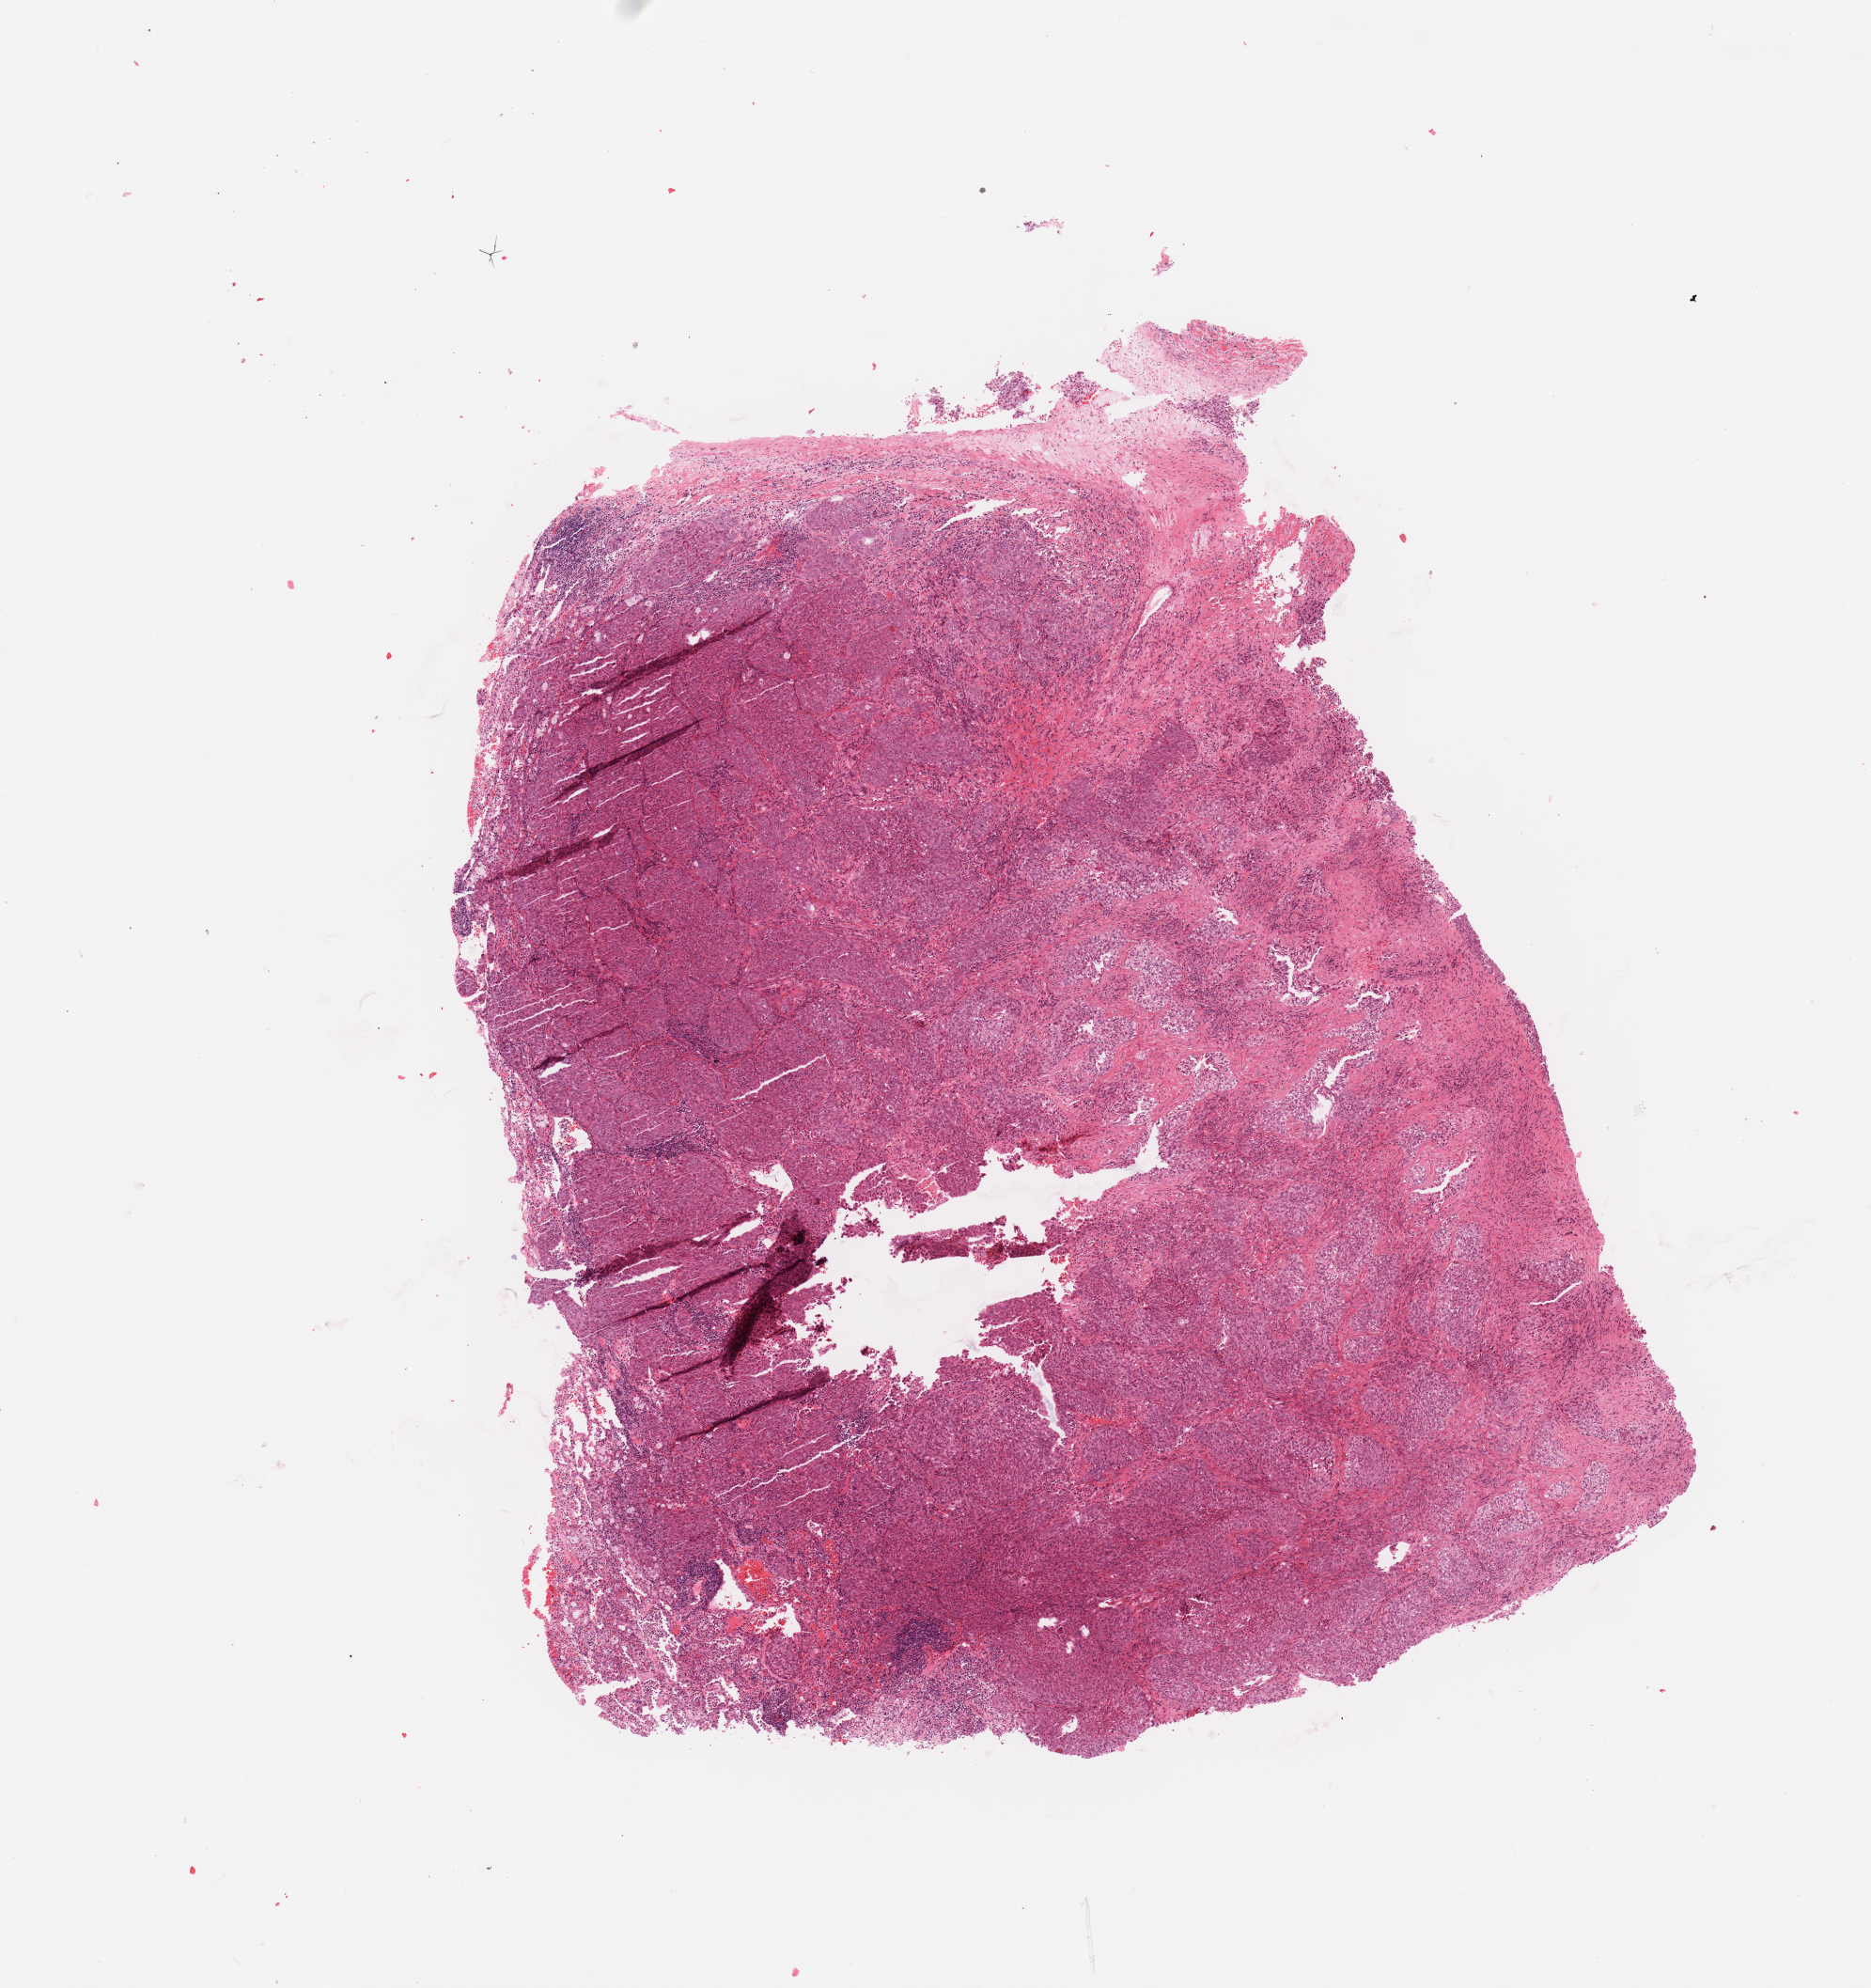
H&E whole-slide image, shown as a low-resolution overview of the whole scanned area (about 7.9 x 8.4 mm, acquisition: 20x scan). Lung, tumour tissue. Patient: female, age 43 years. Histologic grade: G3 (poorly differentiated).
• diagnosis: Adenocarcinoma, NOS
• AJCC pathologic stage: IIIA